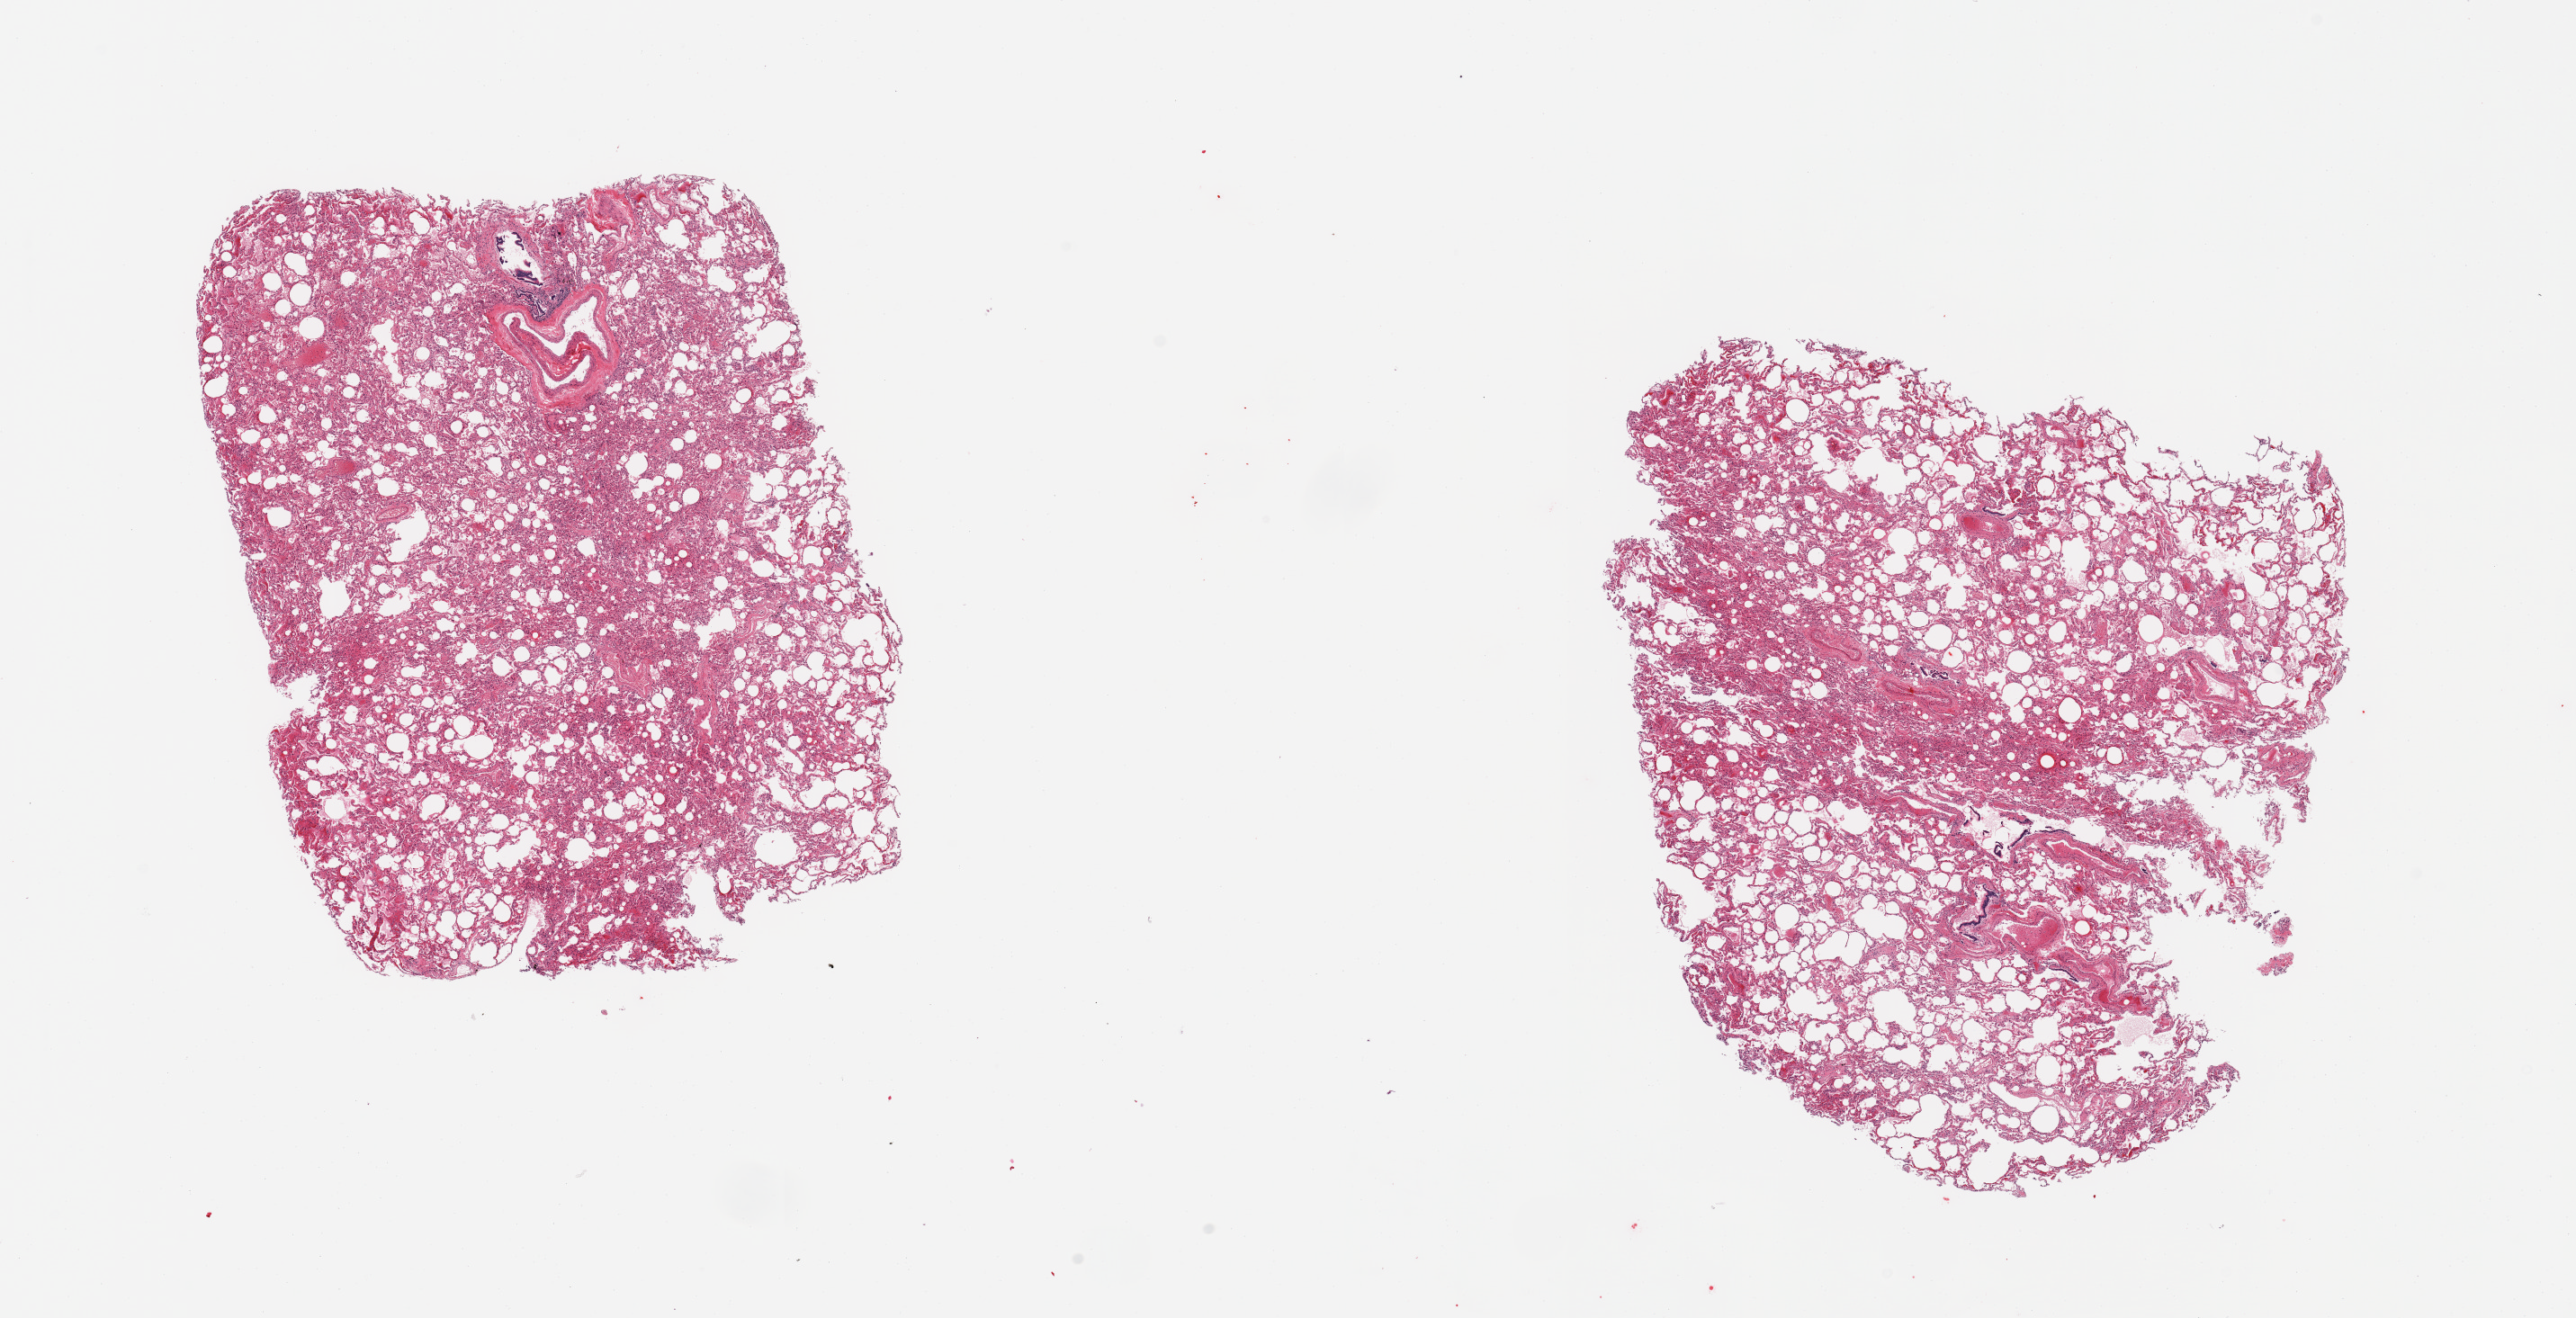
Digitized H&E-stained section — shown as a low-resolution overview of the whole scanned area (about 22.6 x 11.6 mm); PAXgene-fixed paraffin-embedded (PFPE) section; target tissue: lung; tissue donor sample. Donor: male.
Pathologist's review note for this sample: 2 pieces; moderate congestion and sloughed bronchial epithelium.